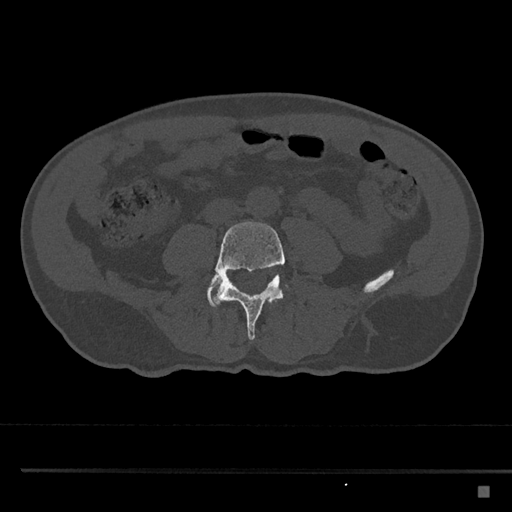
CT including the spine, one axial slice; position 632 of 797 along the scan axis; reconstruction kernel Br40s/3; bone window (W 1800 / L 400 HU); 512 × 512 image matrix, field of view 391 × 391 mm. Male patient, age 59 years. Case-level facts recorded for this patient, not image findings: primary cancer: prostate.
Structures marked on this image (semi-automatic segmentation, software-assisted and operator-edited):
- L4 vertebra: bounding box [x1, y1, x2, y2] px = [213, 221, 287, 340]
- L5 vertebra: [207, 275, 289, 308]